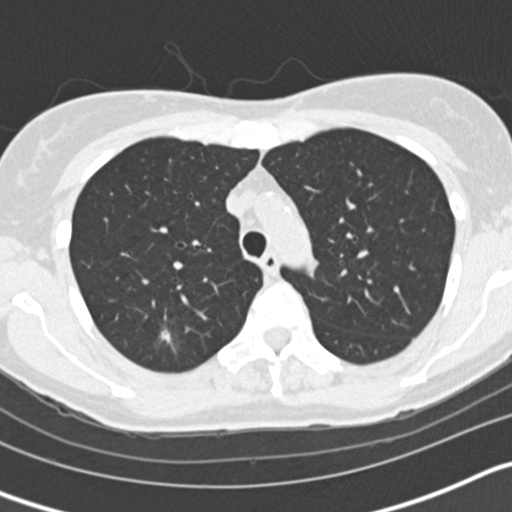
Low-dose screening chest CT, one axial slice; slice 119 of 163 in the series (ordered by position); 120 kVp; lung window (W 1500 / L -600 HU); 512 × 512 image matrix.
Outlined on this slice (manually delineated by an expert):
- lesion 1 (tumor, upper lobe of right lung): box from (x=160, y=330) to (x=171, y=343) px